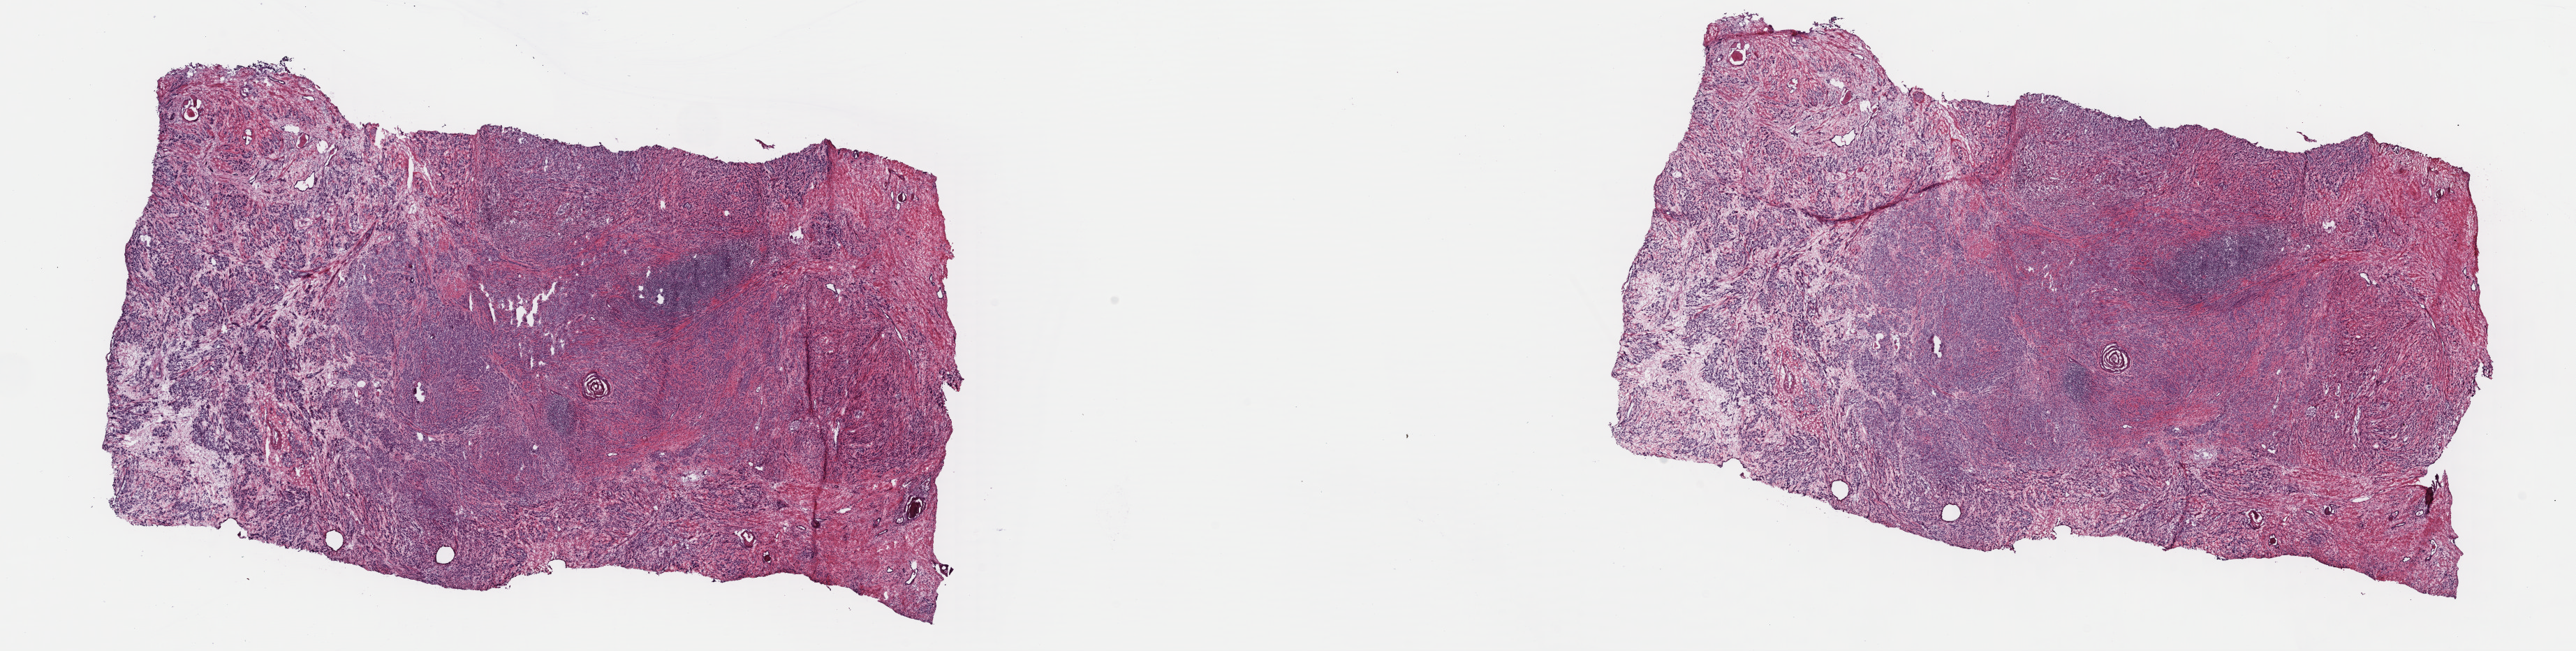
H&E whole-slide image — whole scanned area (about 29.1 x 7.4 mm) shown as a low-resolution overview; frozen section from the top of the tissue portion; sample: primary tumour, prostate. Male, age 56 years at initial diagnosis. Gleason score: 9 (5+4). Pathologist review of this section (percent, as recorded): tumour cells 75%, tumour nuclei 80%, normal cells 0%, stromal cells 25%, necrosis 0%. Infiltration values recorded for this section: lymphocyte infiltration 0%, monocyte infiltration 0%, neutrophil infiltration 0%.
Laterality: bilateral. Lymph nodes positive (case pathology): 0 of 13 examined. Histologic diagnosis: Adenocarcinoma, NOS (prostate gland).